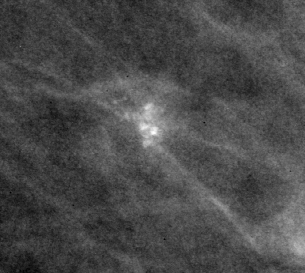
Cropped region of a digitized screen-film mammogram centred on a radiologist-marked abnormality, left breast, MLO view.
Finding: calcifications, morphology pleomorphic, distribution clustered; BI-RADS assessment category 4; pathology result (as recorded, not read from the image): benign.